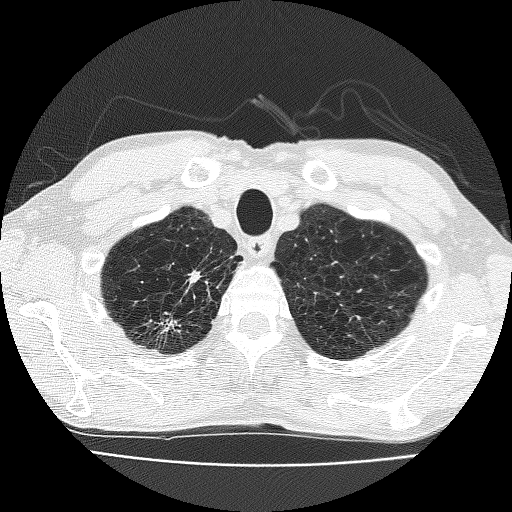
Axial slice from a low-dose chest CT screening exam; third screening round (two years after baseline); lung window (W 1500 / L -600 HU); 2 mm slice thickness; lung (sharp) reconstruction kernel (FC51); slice 32 of 185 in the series. Male participant, aged 63 years at enrolment. Current smoker at enrolment.
• Expert-annotated lung lesion, bounding box (x1, y1, x2, y2) in pixels: (142, 256, 221, 342).
• Screening reader's record for this exam (one nodule recorded; not confirmed to be the boxed lesion): non-calcified nodule or mass ≥4 mm, right upper lobe, 17 × 10 mm, spiculated (stellate) margins, soft tissue attenuation, pre-existing on the prior screen: yes; interval growth: yes.